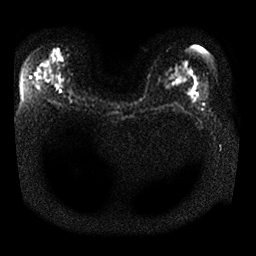
Breast MRI, one axial slice; position 19 of 25 along the scan axis; diffusion-weighted series; image 2 of 4 stored at this slice position (different b-values; order by instance number); 1.5 T; 4 mm slice thickness; 256 × 256 image matrix. Female patient.
Structures marked on this image (outlined manually by an expert reader):
- tumour on diffusion-weighted imaging: box from (x=51, y=48) to (x=64, y=60) px